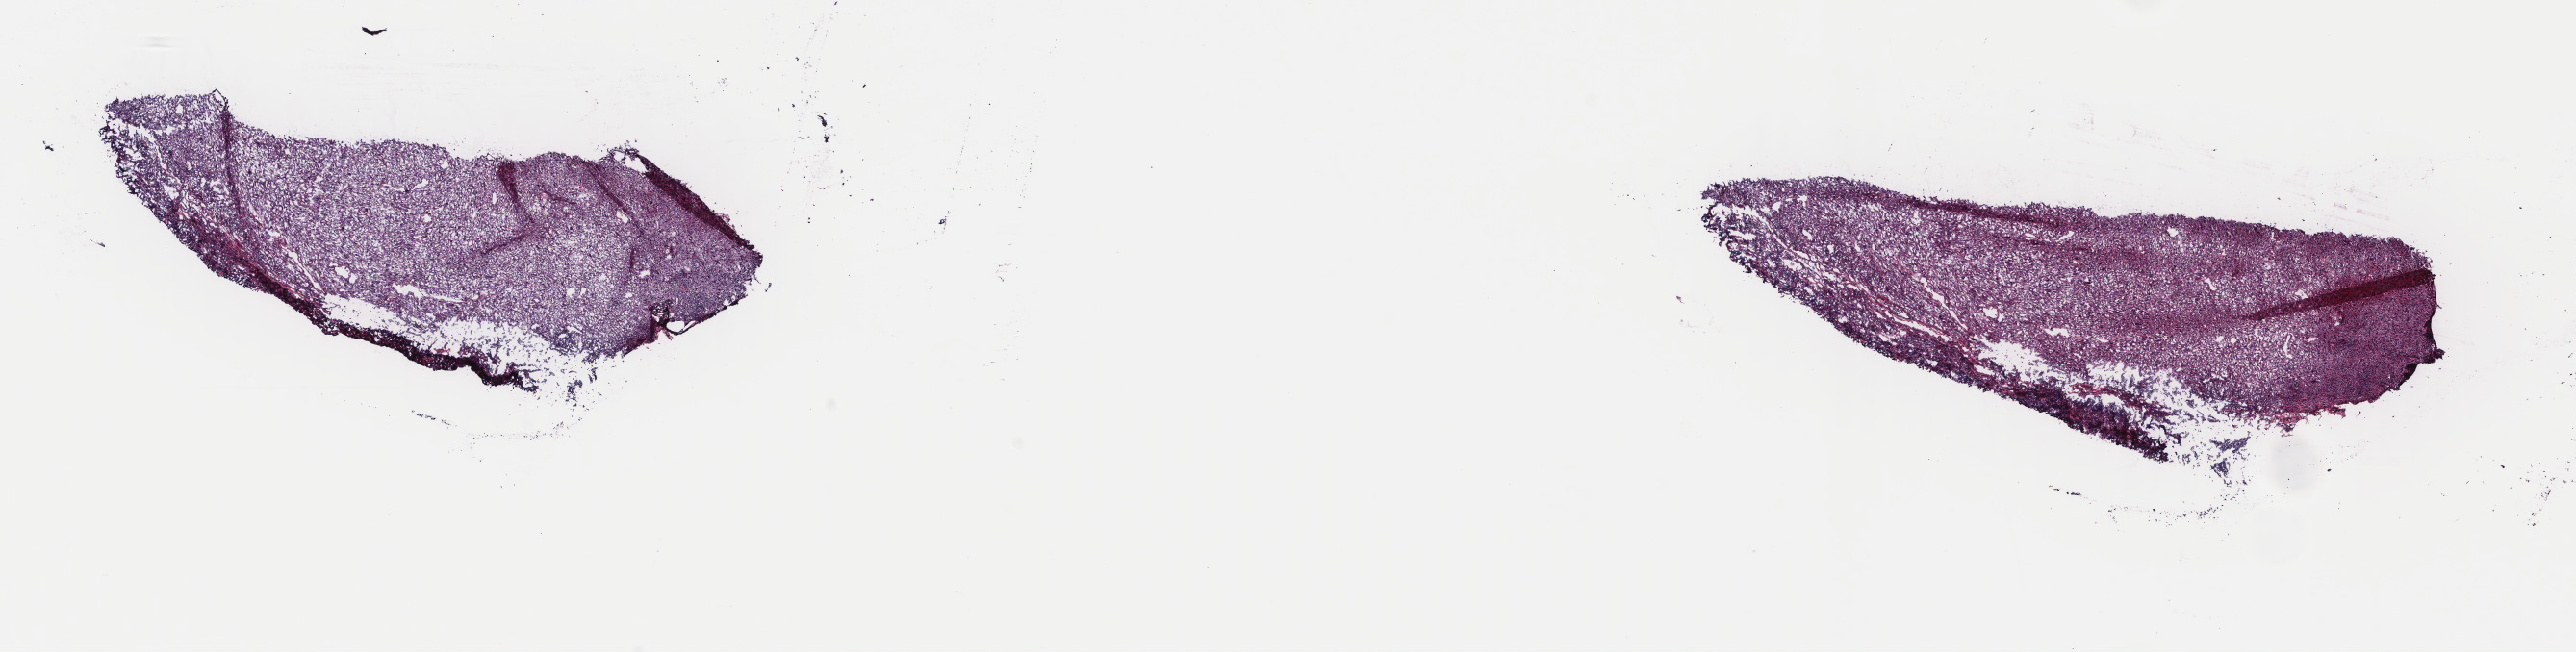
Whole-slide histology image, H&E-stained, low-resolution overview of the scanned area, about 21.2 x 5.4 mm (from a 40x scan); frozen section from the top of the tissue portion; metastatic tumour sample, sampled site: pelvic lymph nodes. Patient: male, age at initial diagnosis 55 years. Composition of this section per pathologist review: tumour cells 100%, tumour nuclei 80%, normal cells 0%, stromal cells 0%, necrosis 0%. Infiltration values recorded for this section: lymphocyte infiltration 2%, monocyte infiltration 1%, neutrophil infiltration 0%.
This section: metastatic tumour tissue. Patient diagnosis: Malignant melanoma, NOS.